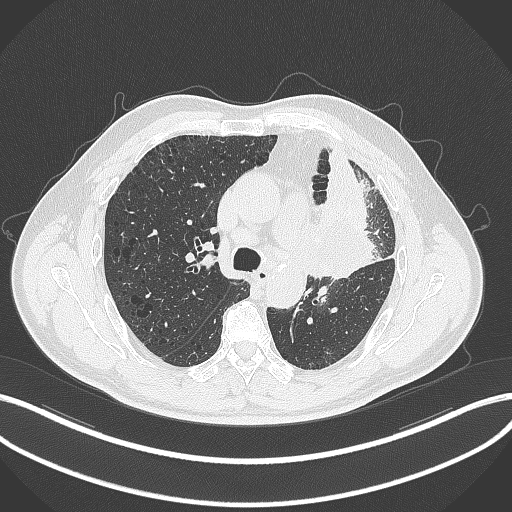
Chest CT, one axial slice. Slice 202 of 297 in the series (ordered by position). Reconstruction kernel B70f. Lung window (W 1500 / L -600 HU). 1 mm slice thickness. 512 × 512 image matrix, field of view 400 × 400 mm. Patient: male, 68 years. Case-level facts recorded for this patient, not image findings: clinical TNM (as recorded): T3 N3 M1.
Structures marked on this image (rectangle marked by the reading radiologist):
- lung tumour (recorded histology: adenocarcinoma): bounding box (x1, y1, x2, y2) in pixels: (304, 193, 385, 284)